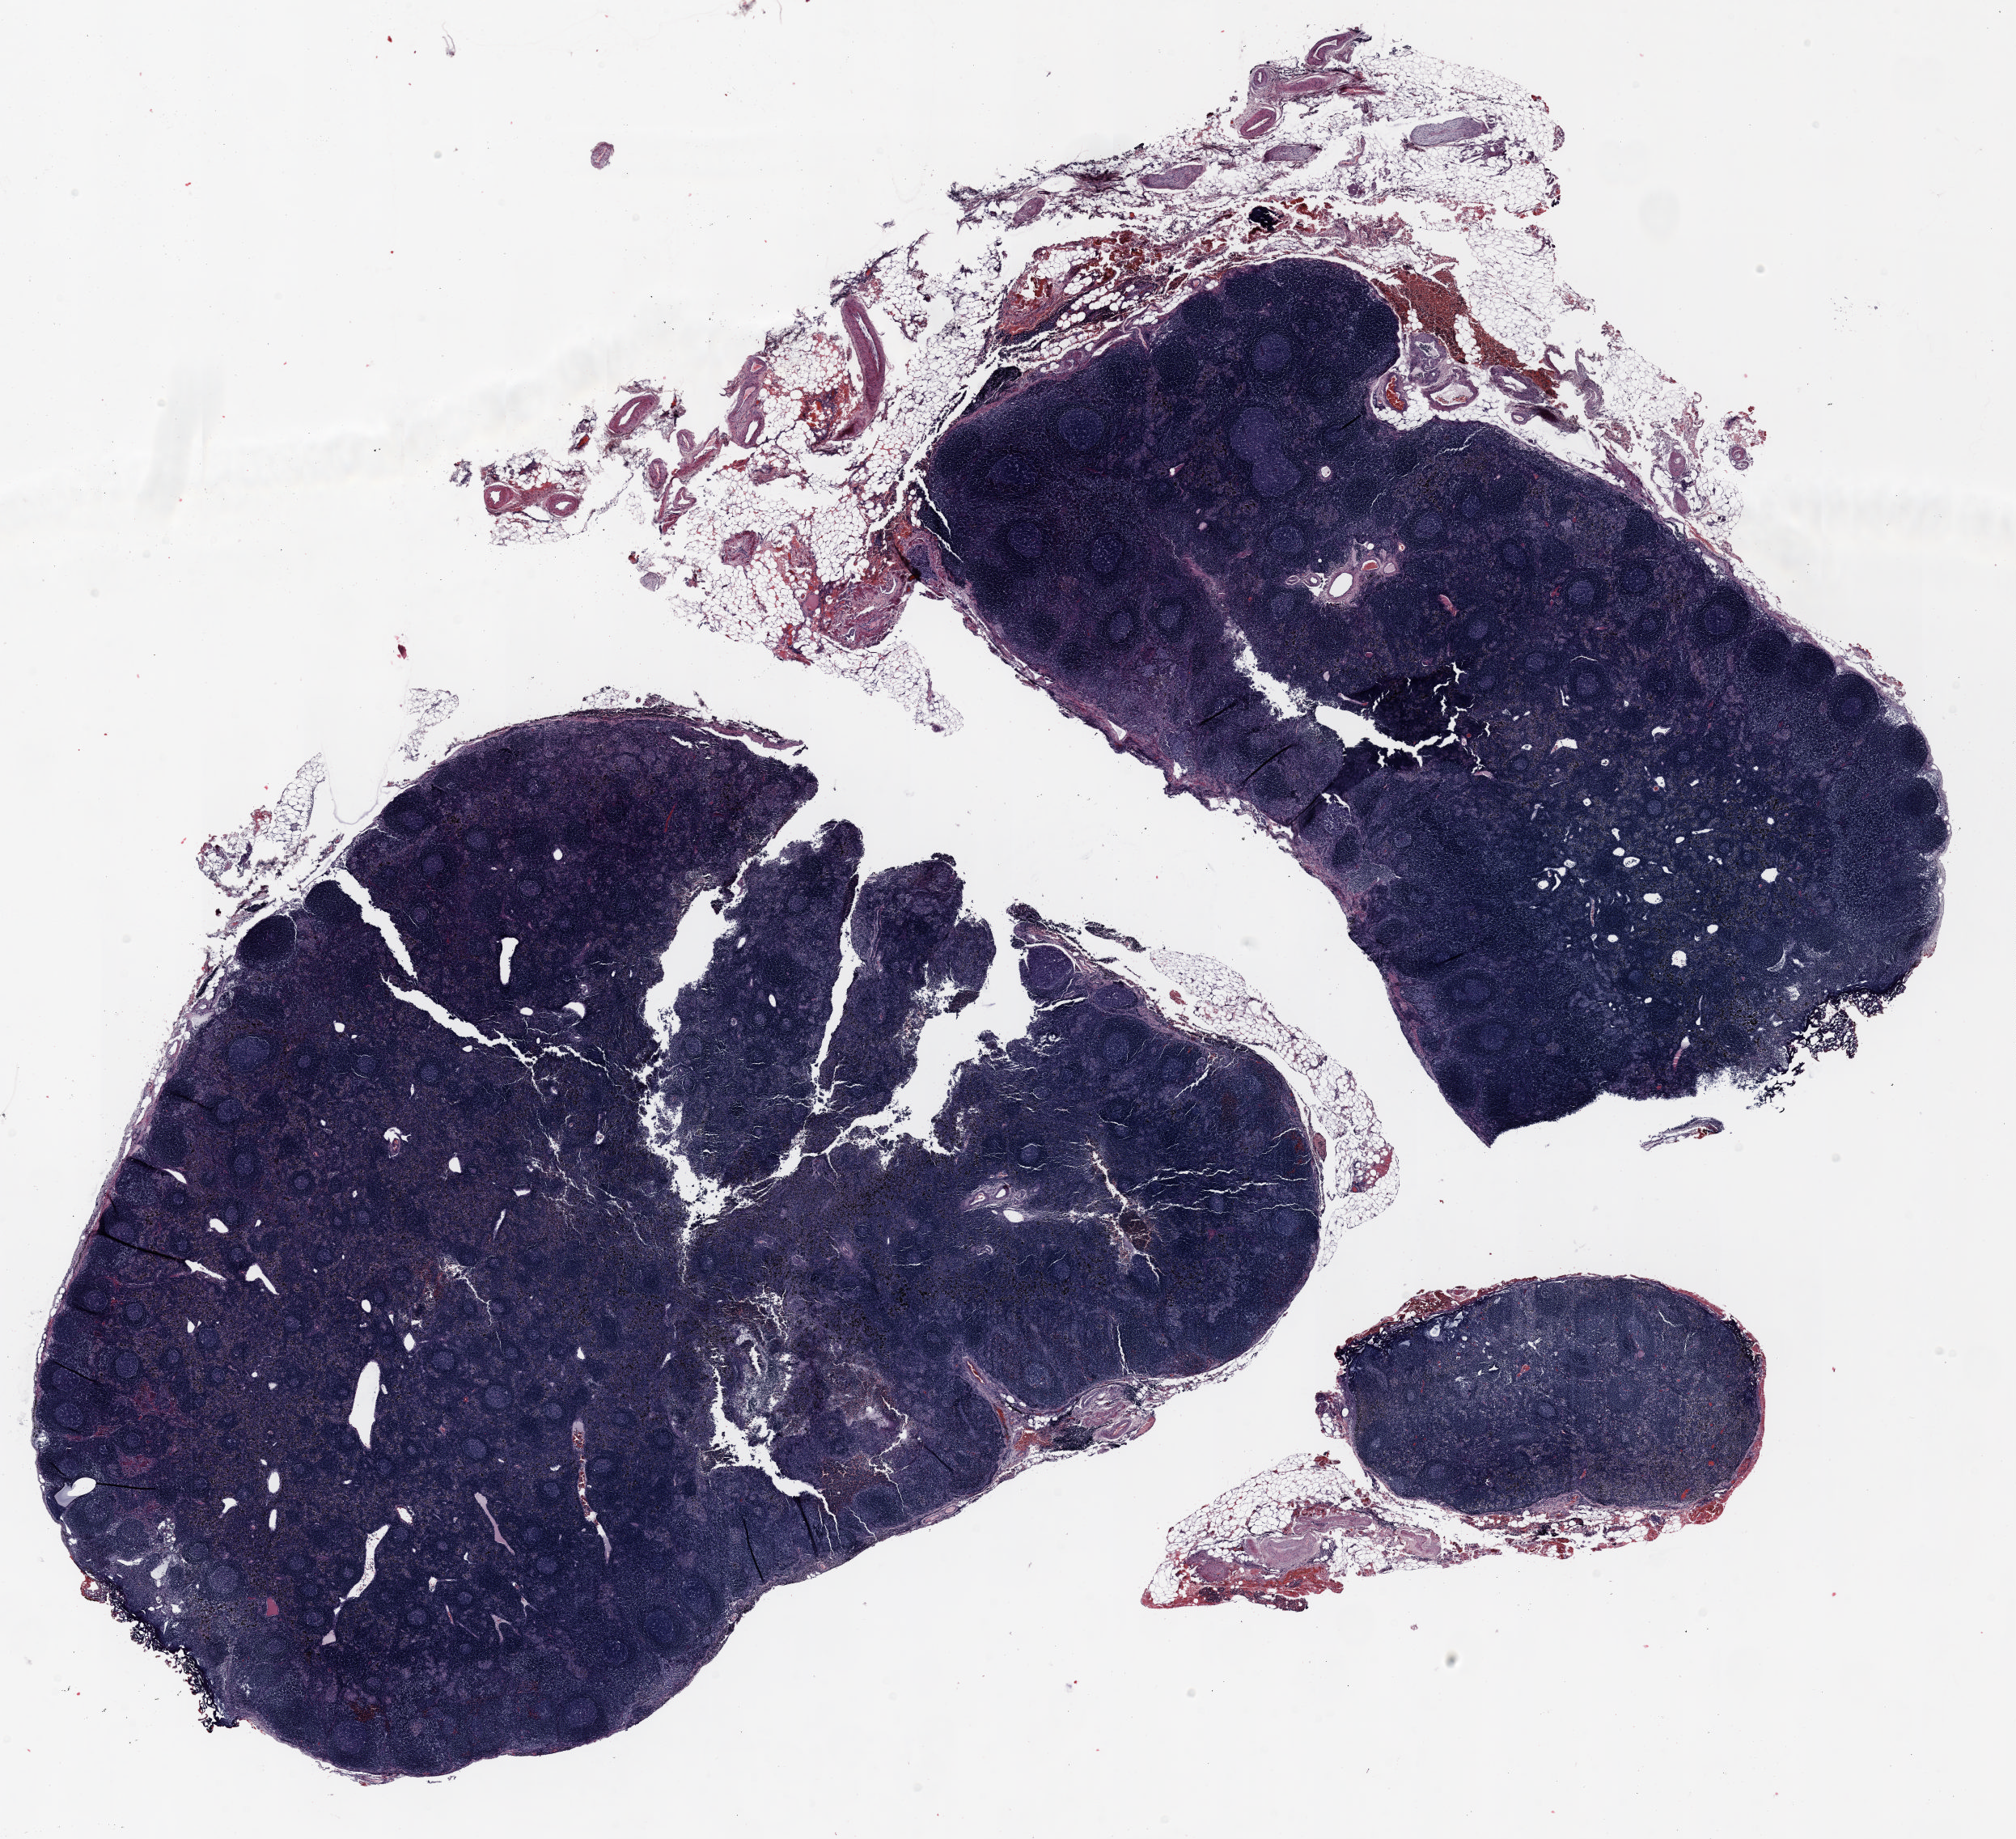
Whole-slide histology image, H&E-stained — a low-resolution overview of the entire scanned area, about 20.0 x 18.3 mm (slide scanned at 20x), formalin-fixed paraffin-embedded (FFPE) section, lung. Male, age 72 at enrolment. Former smoker at enrolment. Grade: moderately differentiated (G2).
• stage (AJCC 6th edition): IIIA
• tumour size (pathology): 53 mm
• participant's lung-cancer diagnosis: Adenosquamous carcinoma
• primary tumour location (clinical record): right upper lobe